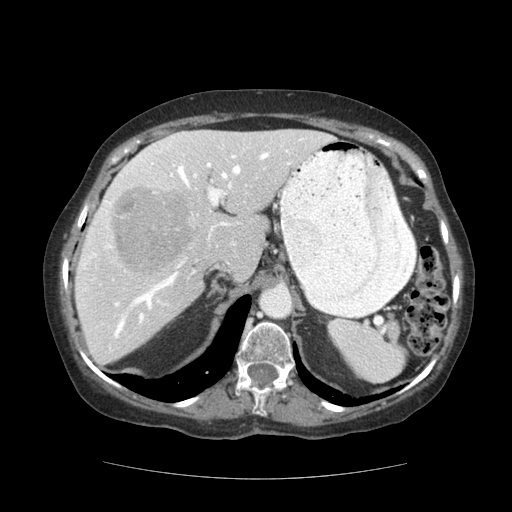
Contrast-enhanced abdominal CT (liver protocol), one axial slice; position 81 of 111 along the scan axis; reconstruction kernel STANDARD; 140 kVp; soft-tissue window (W 400 / L 40 HU); 2.5 mm slice thickness; 512 × 512 image matrix, field of view 360 × 360 mm. From the clinical record (not read from this slice): diagnosis: hepatocellular carcinoma (patient treated with transarterial chemoembolisation; whether this scan precedes or follows treatment is not stated here); TNM stage (as recorded): Stage-I; Child-Pugh class: A.
Outlined on this slice (semi-automatic segmentation, software-assisted and operator-edited):
- liver parenchyma outside the tumour (the mass and vessels are separate outlines, so this box may not span the whole liver): box from (x=74, y=130) to (x=332, y=364) px
- mass: (x=113, y=184)–(x=193, y=273)
- liver vessels: (x=81, y=136)–(x=304, y=338)